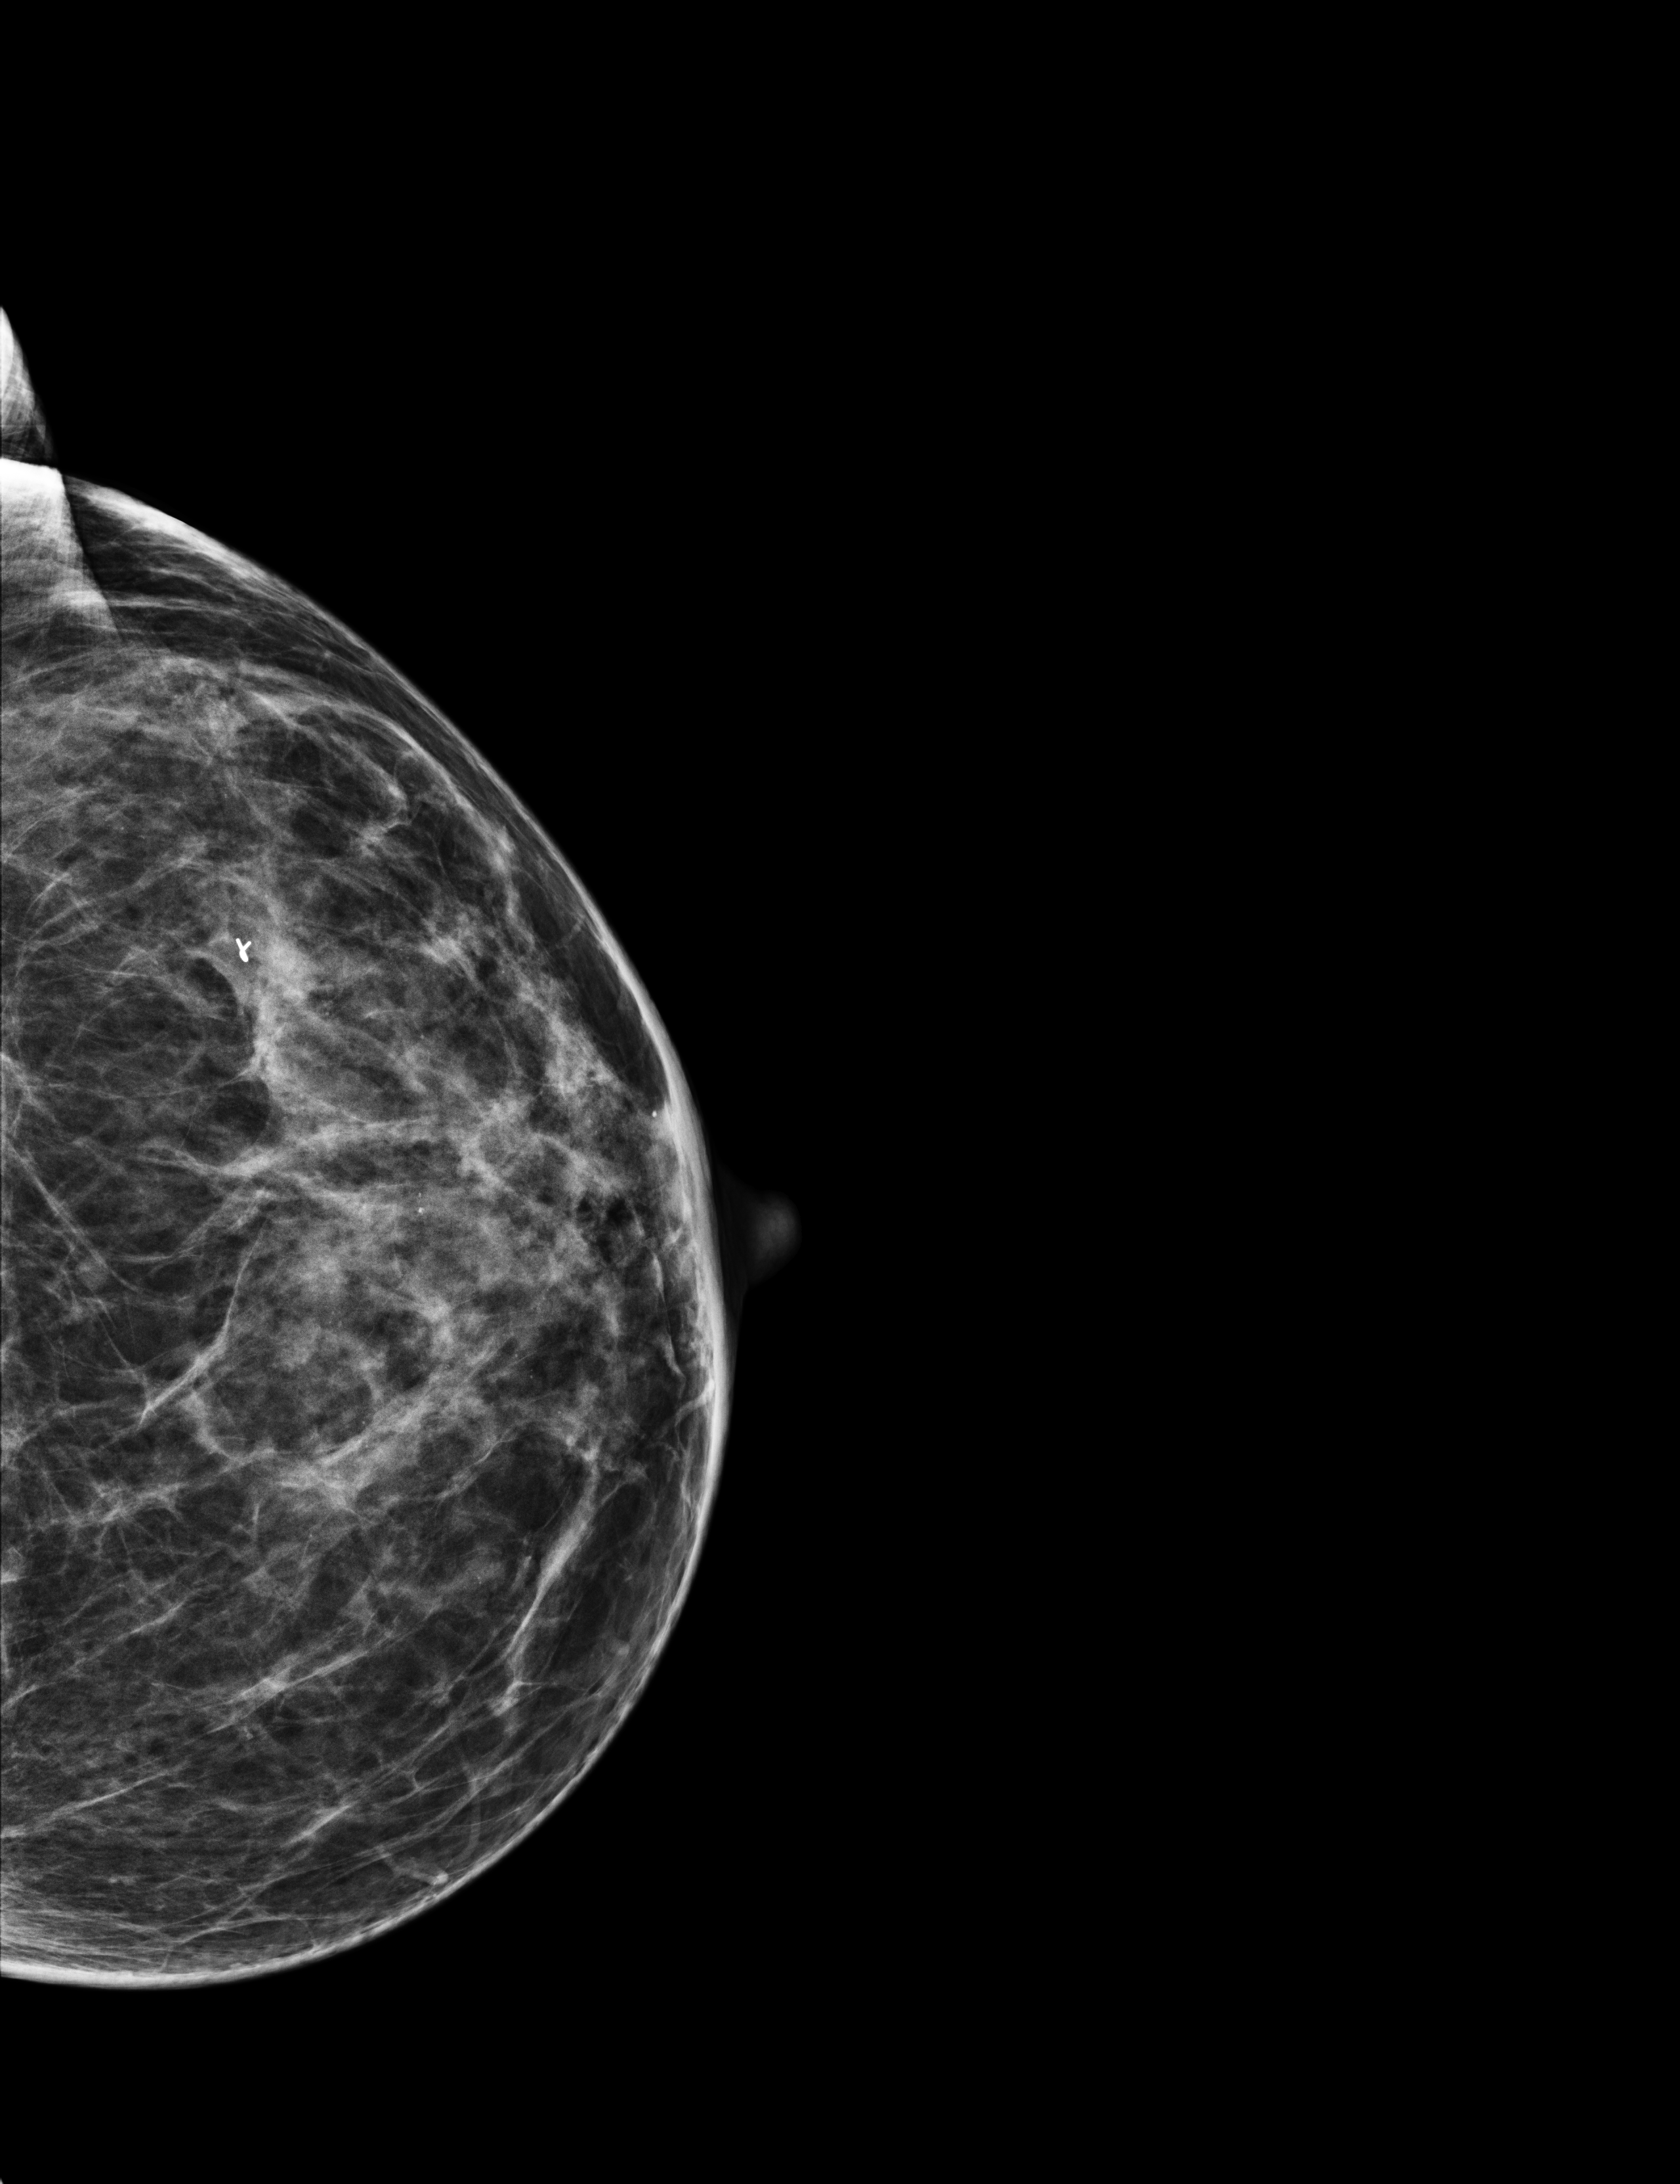
Diagnostic examination (additional views); compressed breast thickness 53 mm. Female patient, age 51 years.
Image type: full-field digital mammogram. Breast: left. Projection: CC view.